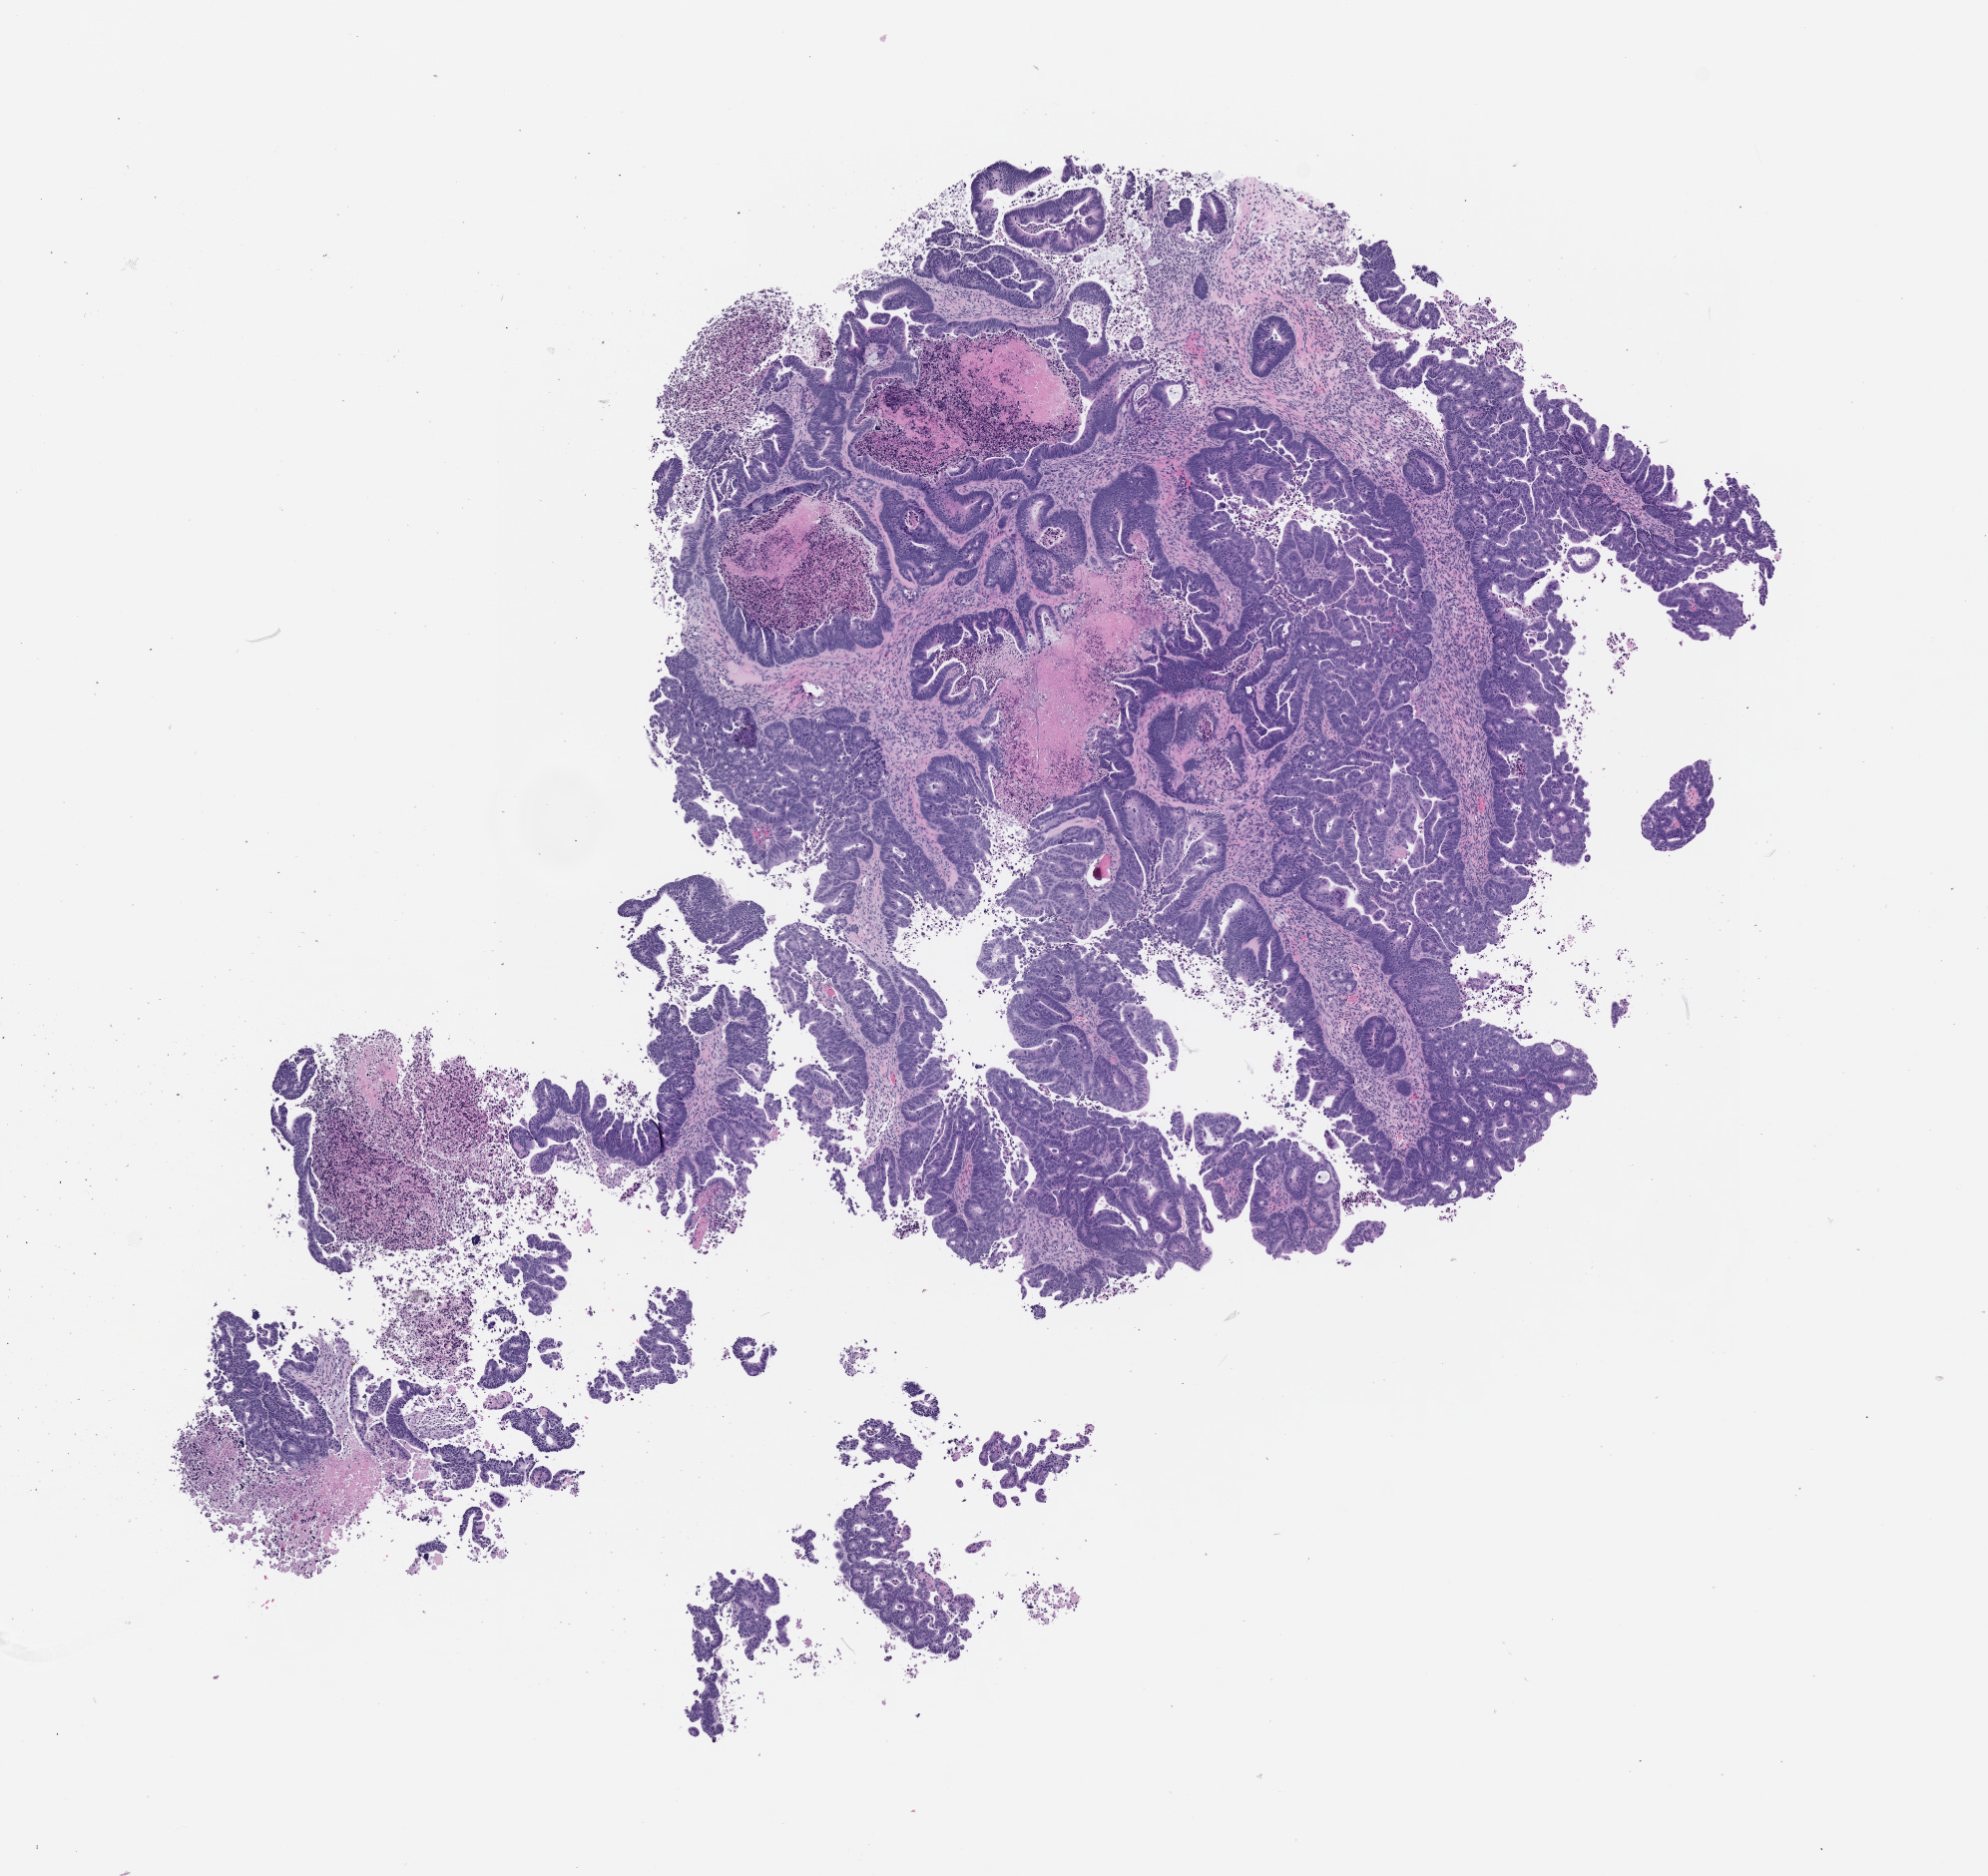
Haematoxylin and eosin whole-slide image of a patient-derived xenograft (PDX) tumor grown in a mouse, passage 1, shown as a low-resolution overview of the whole scanned area (about 8.0 x 7.6 mm), formalin-fixed, paraffin-embedded (FFPE) tissue, tumor site category: colon.
Originating patient diagnosis: Colon Adenocarcinoma.